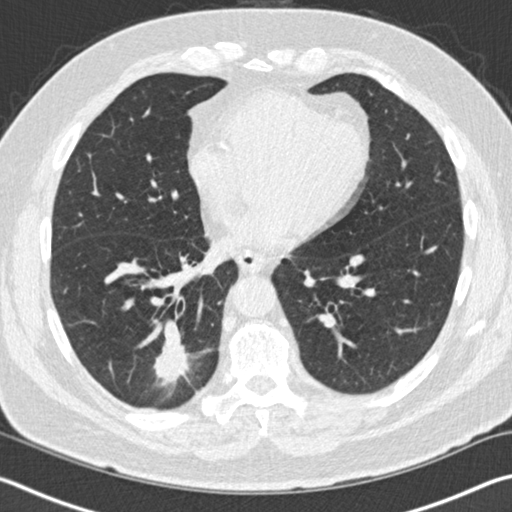
Low-dose screening chest CT, one axial slice; slice 45 of 141 in the series (ordered by position); reconstruction kernel B30f; 120 kVp; lung window (W 1500 / L -600 HU); 512 × 512 image matrix.
Annotated regions visible in this slice (expert manual segmentation):
- lesion 1 (tumor, lower lobe of right lung): box from (x=154, y=322) to (x=191, y=381) px